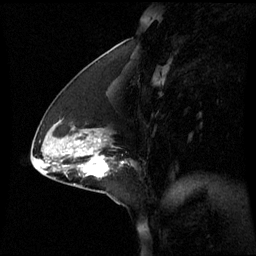
Breast MRI (dynamic contrast-enhanced), one sagittal slice. Dynamic contrast-enhanced series, image 2 of 3 at this slice position (ordered by acquisition). 1.5 T. TE 4.2 ms, TR 8.9 ms. 256 × 256 image matrix, field of view 240 × 240 mm. Female patient, age 44 years. From the clinical record (not read from this slice): setting: breast cancer imaged before/during neoadjuvant chemotherapy; receptor status: triple-negative.
Annotated regions visible in this slice (semi-automatically segmented with operator editing):
- analysis volume of interest (the breast-tissue region the enhancement analysis was run in; not a lesion): bounding box [x1, y1, x2, y2] px = [76, 150, 127, 177]
- tumour enhancement mask (voxels above the 70 % enhancement threshold inside the analysis volume of interest): [88, 158, 109, 177]